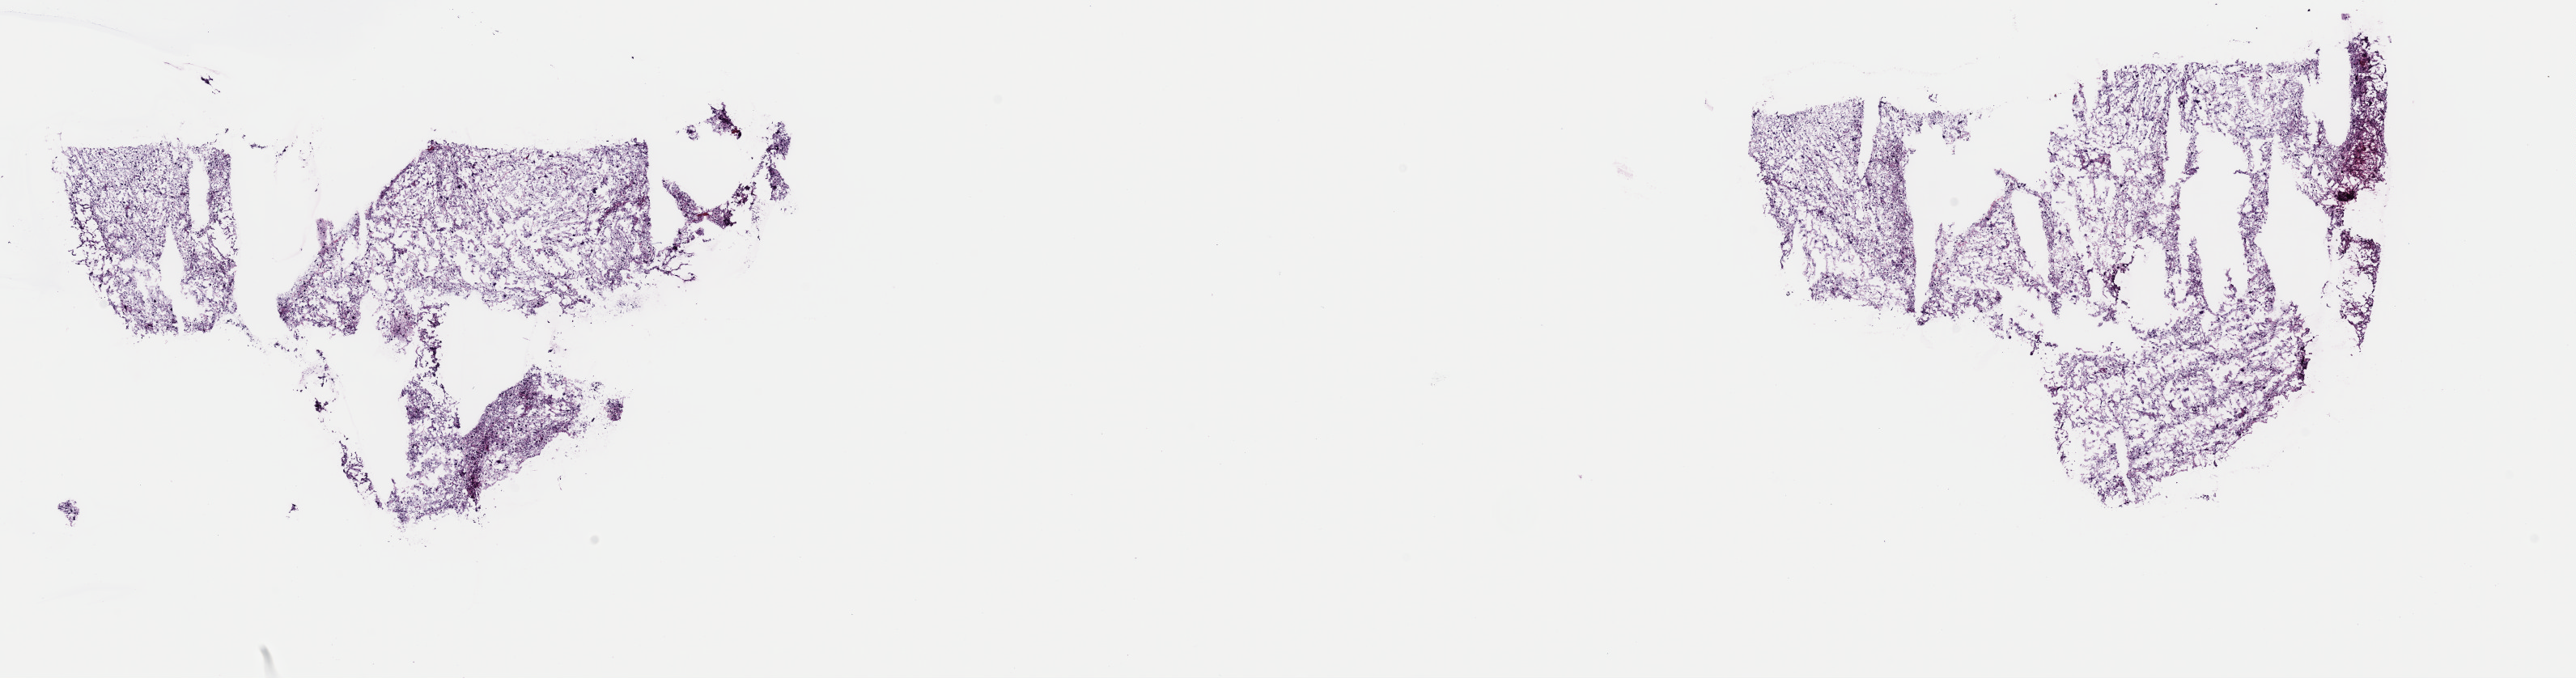
Whole-slide histology image, H&E, a low-resolution overview of the entire scanned area, about 25.1 x 6.6 mm (acquisition: 40x scan); frozen section from the top of the tissue portion; connective, subcutaneous and other soft tissues, primary tumour sample. Male, age 74 years at initial diagnosis. Composition of this section per pathologist review: tumour cells 100%, tumour nuclei 80%, normal cells 0%, stromal cells 0%, necrosis 0%. Inflammatory infiltration, as recorded: lymphocyte infiltration 1%, monocyte infiltration 0%, neutrophil infiltration 0%.
Diagnosis: Fibromyxosarcoma (connective, subcutaneous and other soft tissues of lower limb and hip).